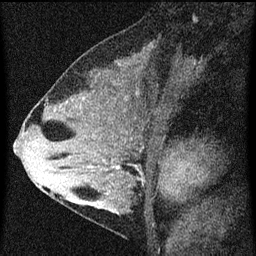
Breast MRI (dynamic contrast-enhanced), one sagittal slice. Position 34 of 60 along the scan axis. Dynamic contrast-enhanced series, image 2 of 3 at this slice position (ordered by acquisition). 1.5 T. TE 4.2 ms, TR 8 ms. 2 mm slice thickness. 256 × 256 image matrix. Patient: female, 33 years.
Annotated regions visible in this slice (semi-automatically segmented with operator editing):
- analysis volume of interest (the breast-tissue region the enhancement analysis was run in; not a lesion): bounding box <67,118,159,215> (left, top, right, bottom; pixels)
- tumour enhancement mask (voxels above the 70 % enhancement threshold inside the analysis volume of interest): <91,166,119,169>